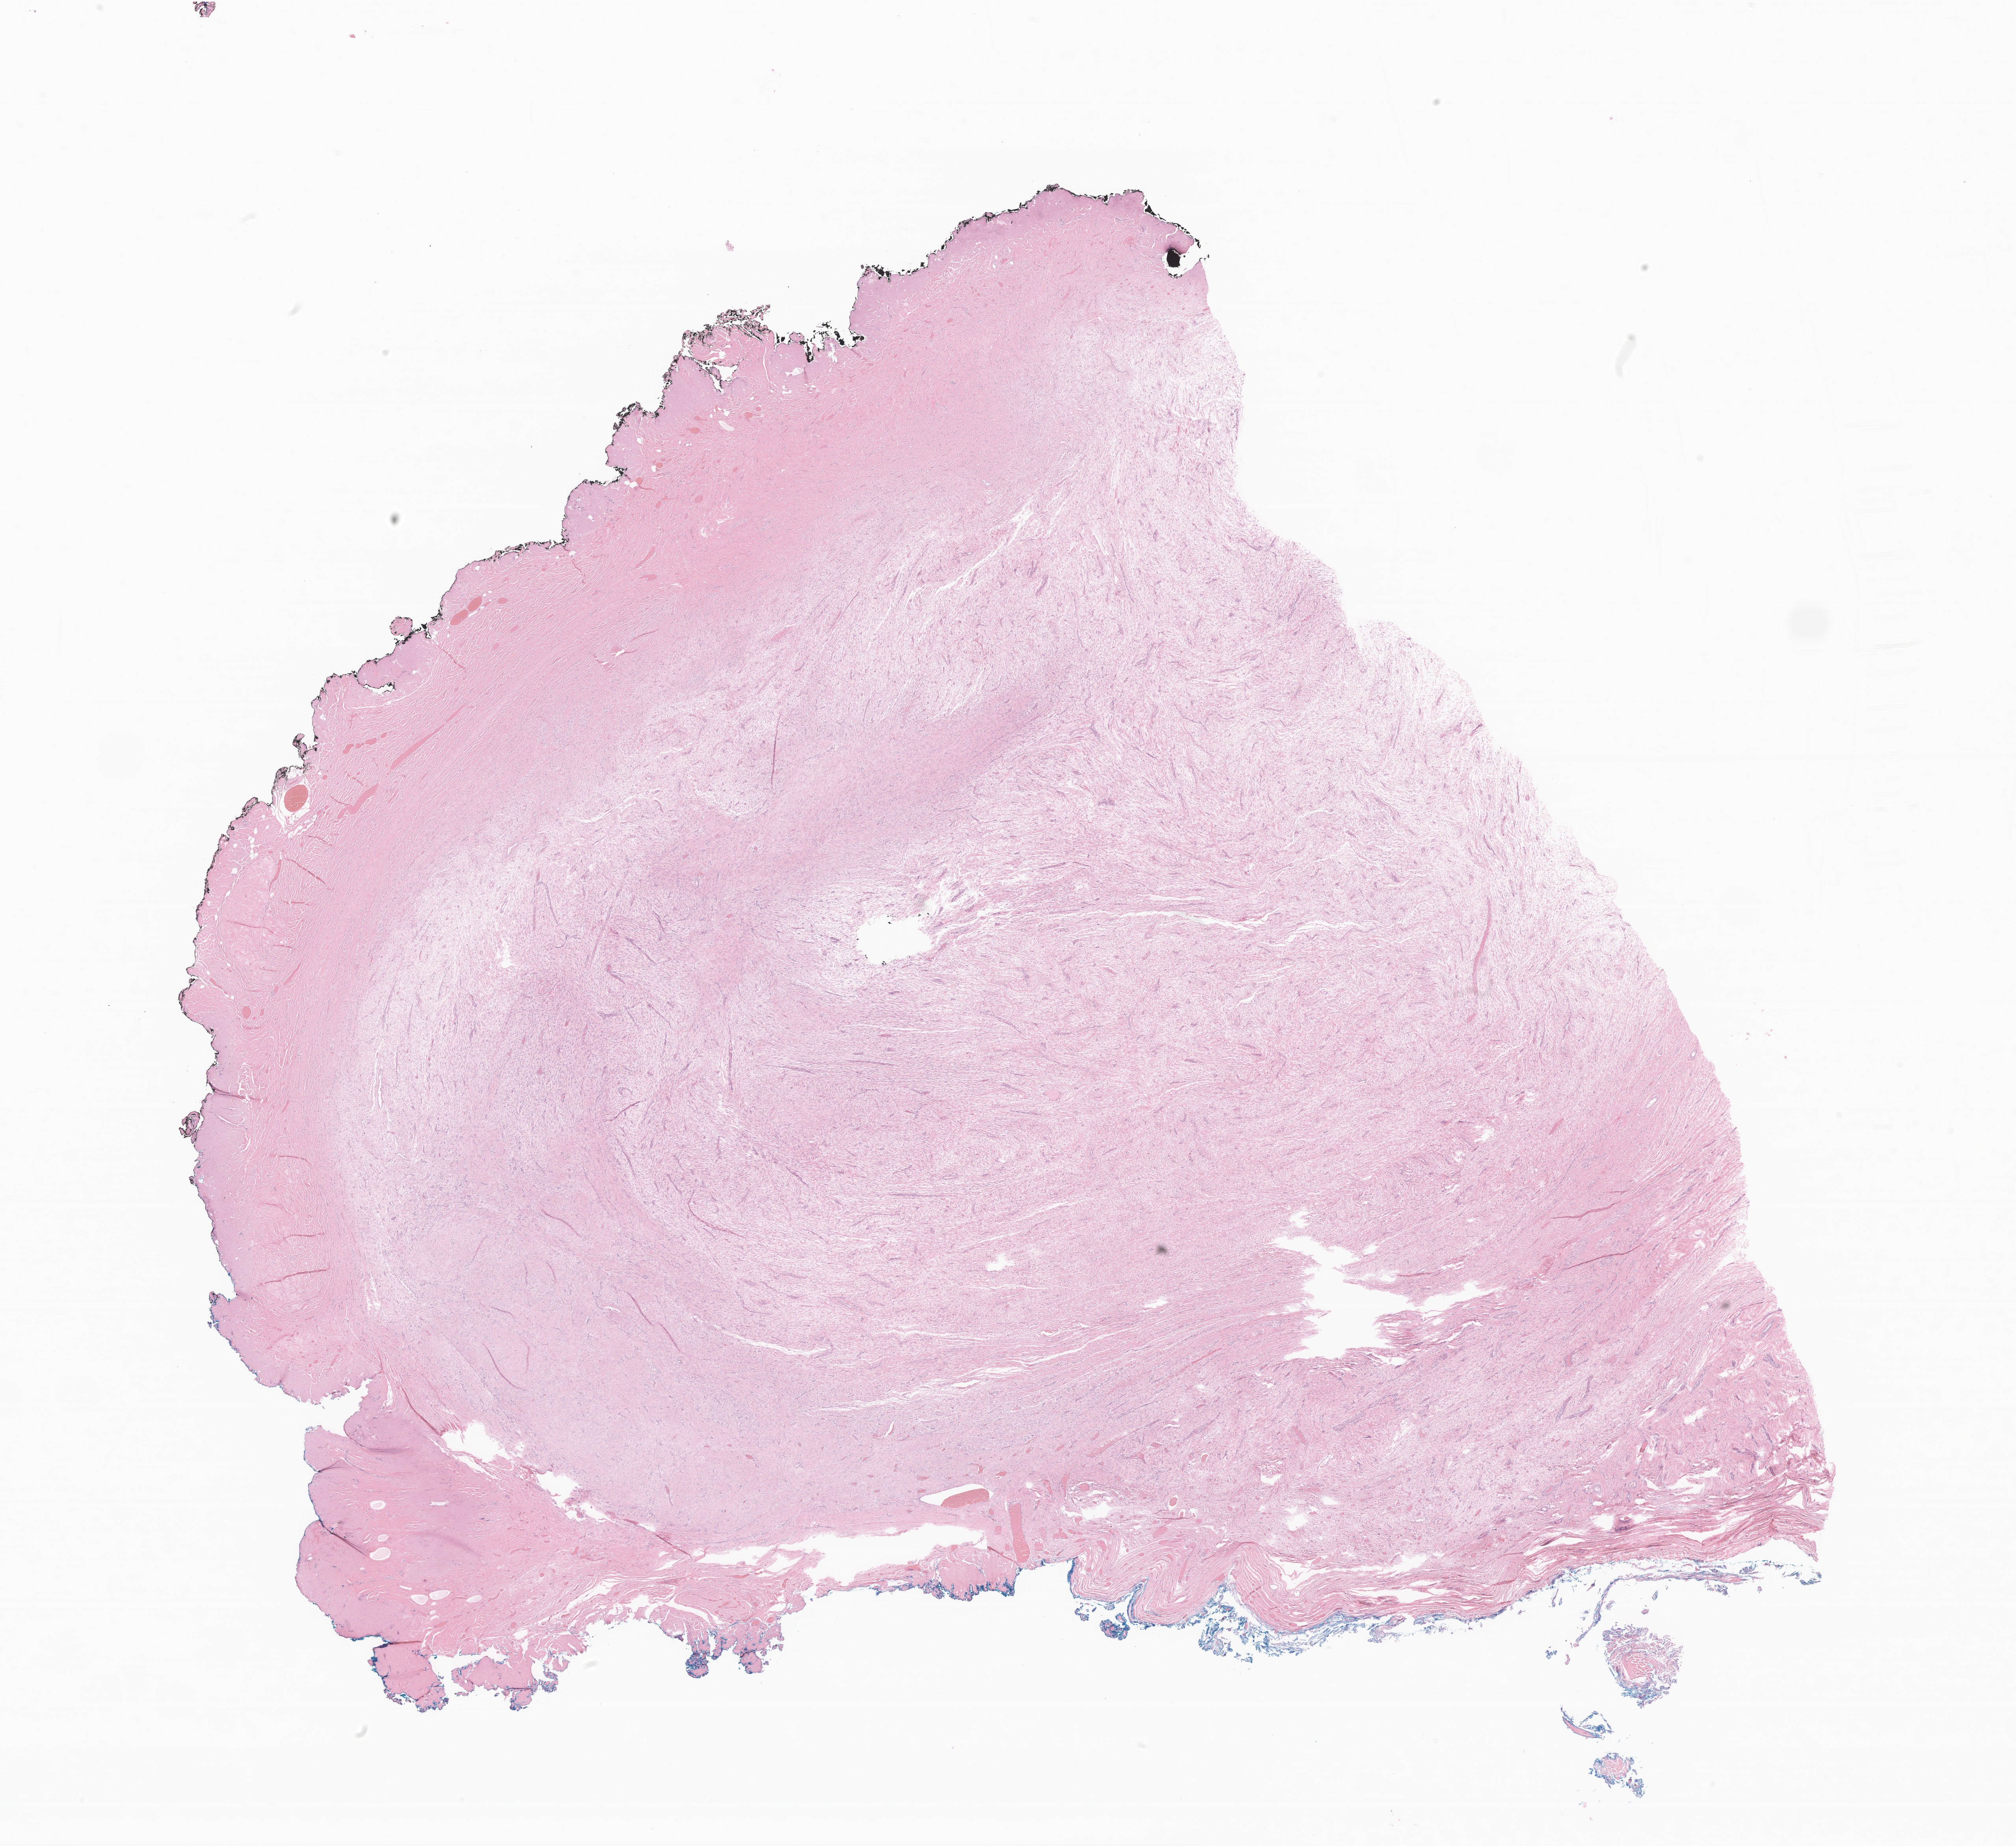
Digitized hematoxylin and eosin (H&E)-stained section of tumor tissue from the head and neck — shown as a low-resolution overview of the whole scanned area (about 21.6 x 19.7 mm). FFPE section. Patient male; age 86 months.
Diagnosis (ICD-O-3 morphology term): Aggressive fibromatosis.